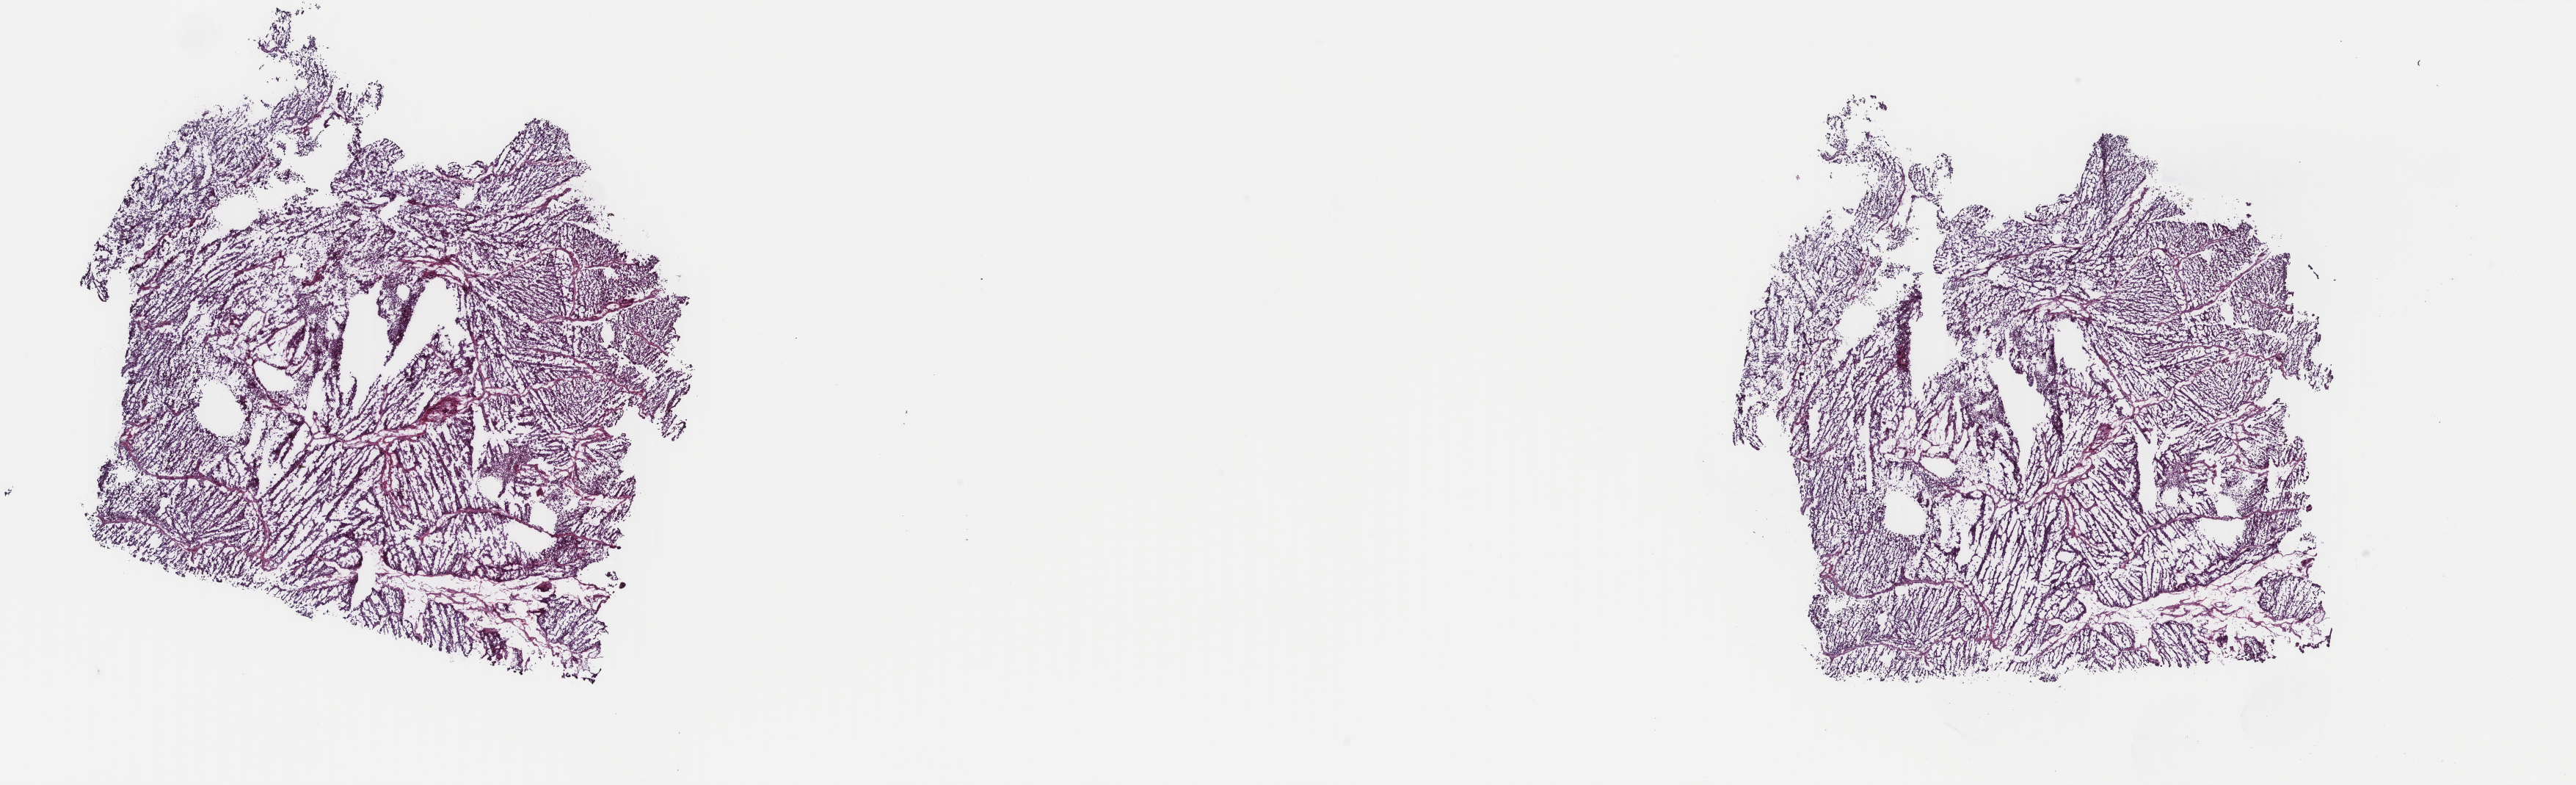
Digitized H&E tissue section (whole slide) — low-resolution overview of the scanned area, about 27.9 x 8.5 mm (slide scanned at 40x), frozen section from the top of the tissue portion, primary tumour sample from the bladder. Male patient; age at initial diagnosis 34 years. Histologic grade: low grade. Slide review estimates, as recorded: tumour cells 90%, tumour nuclei 90%, normal cells 0%, stromal cells 10%, necrosis 0%. Infiltration values recorded for this section: lymphocyte infiltration 2%, monocyte infiltration 1%, neutrophil infiltration 1%.
- diagnosis: Papillary transitional cell carcinoma
- AJCC pathologic stage: III (7th edition)